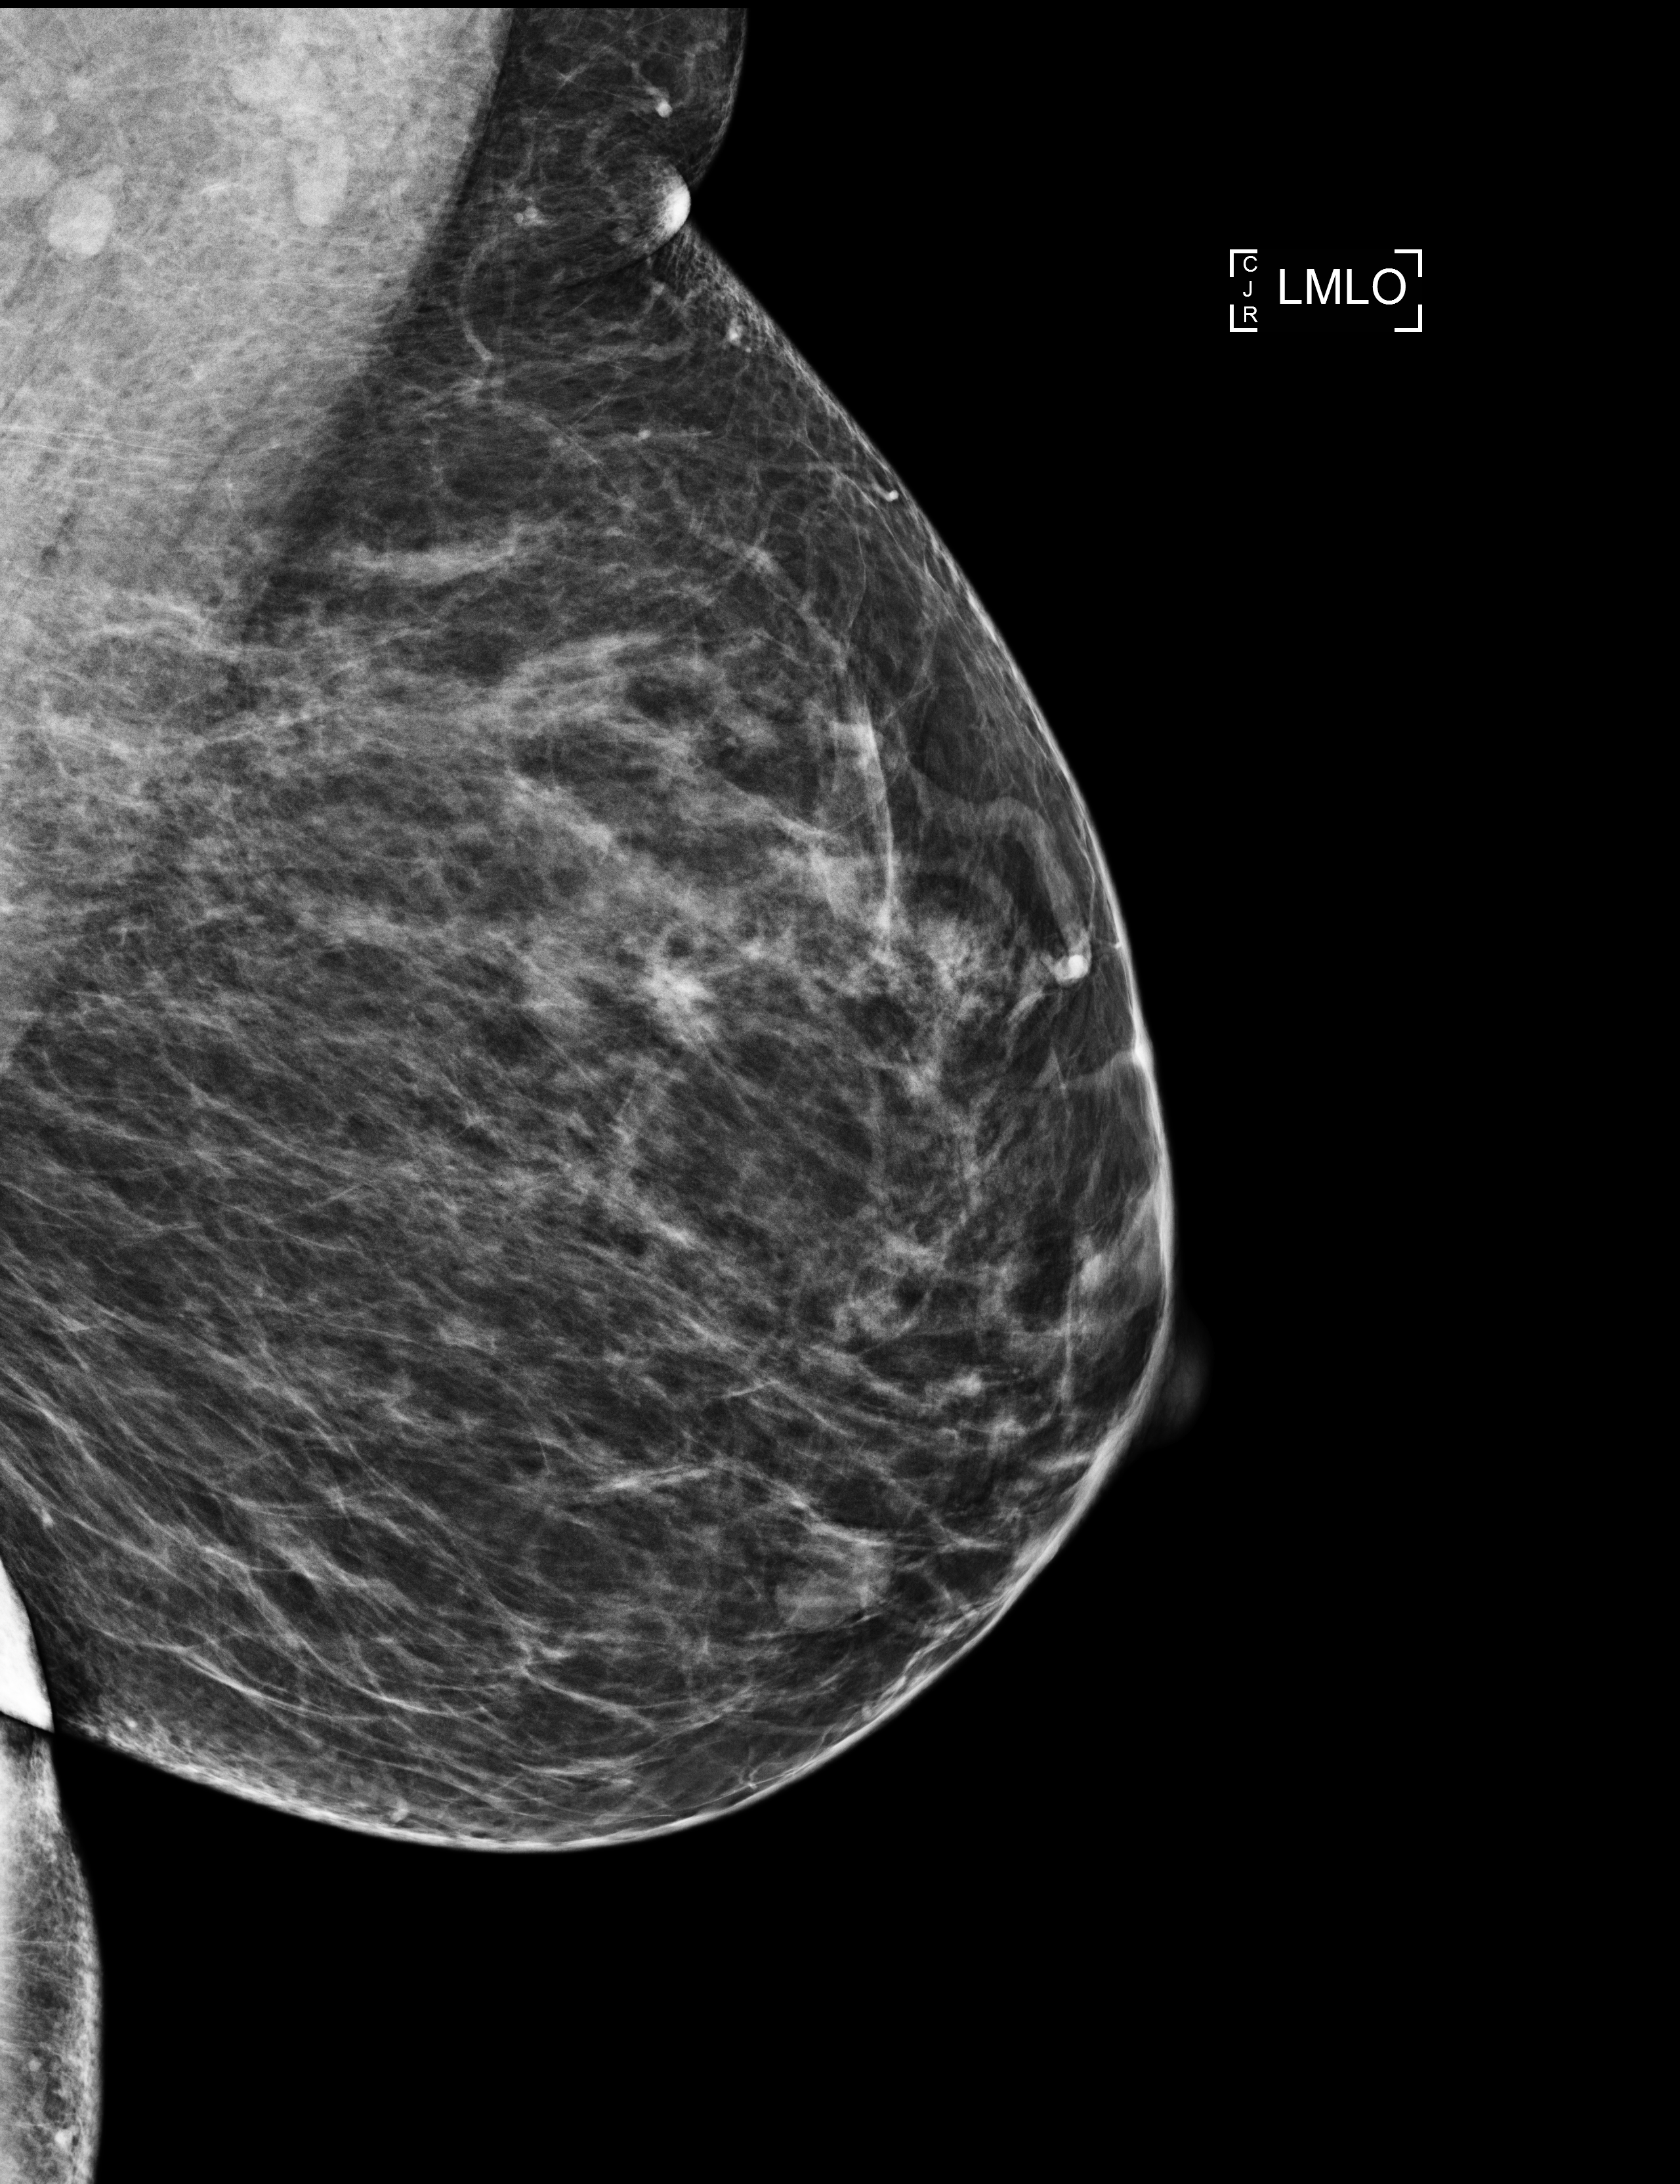
Full-field digital mammogram (FFDM); left breast; mediolateral oblique (MLO) view; annual screening mammography examination; compressed breast thickness 68 mm; system: Selenia Dimensions. Patient aged 44 years (female).
- BI-RADS breast density category at the screening exam (both breasts, scale 1–4): 3
- final BI-RADS assessment for this screening round (tomosynthesis exam, both breasts): category 2
- recall: no recall after this screen